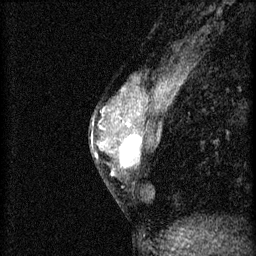
Breast MRI (dynamic contrast-enhanced), one sagittal slice; position 26 of 46 along the scan axis; 3 images stored at this slice position (order not interpretable as contrast timing); 1.5 T; TE 4.2 ms, TR 8.2 ms; 2 mm slice thickness; 256 × 256 image matrix, field of view 180 × 180 mm. Female patient, age 44 years.
Annotated regions visible in this slice (semi-automatically segmented with operator editing):
- analysis volume of interest (the breast-tissue region the enhancement analysis was run in; not a lesion): box from (x=110, y=128) to (x=156, y=181) px
- tumour enhancement mask (voxels above the 70 % enhancement threshold inside the analysis volume of interest): (x=112, y=134)–(x=144, y=175)